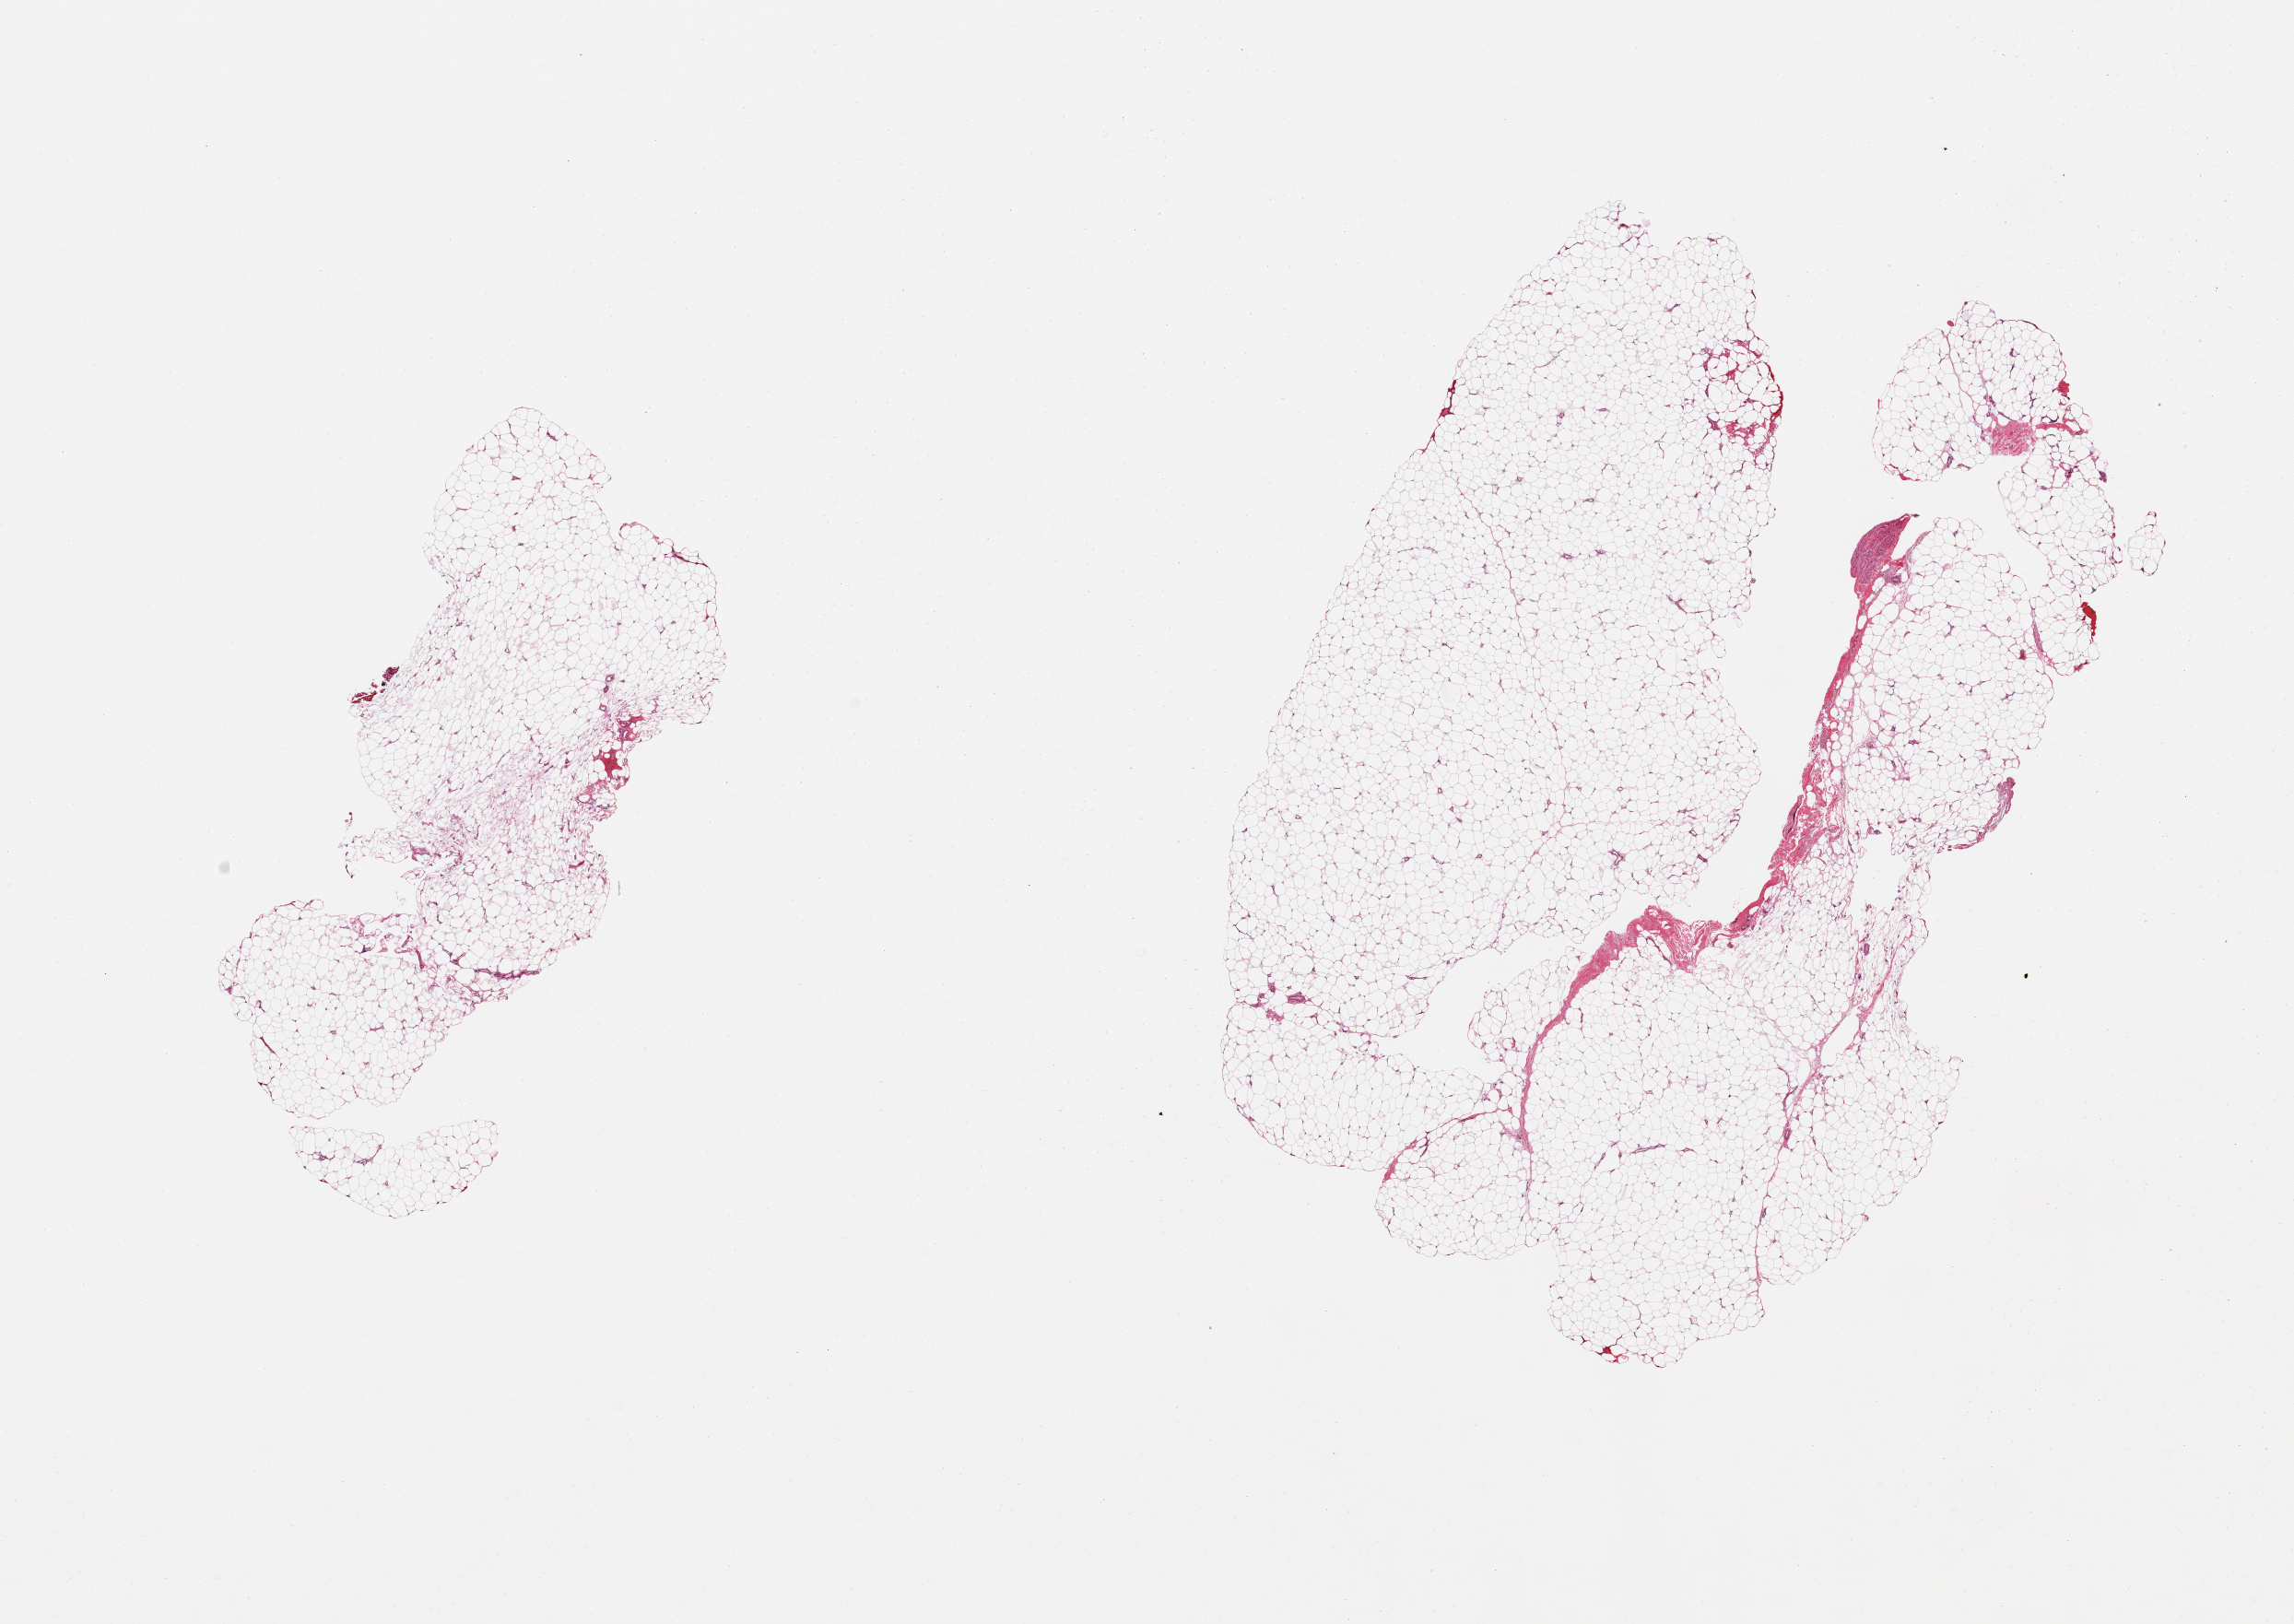
Digitized H&E-stained section — whole scanned area (about 19.7 x 13.9 mm) shown as a low-resolution overview, PAXgene-fixed, paraffin-embedded tissue, section of adipose tissue (target tissue), tissue donor sample.
• pathologist's review note for this sample: 2 pieces, trace fascia